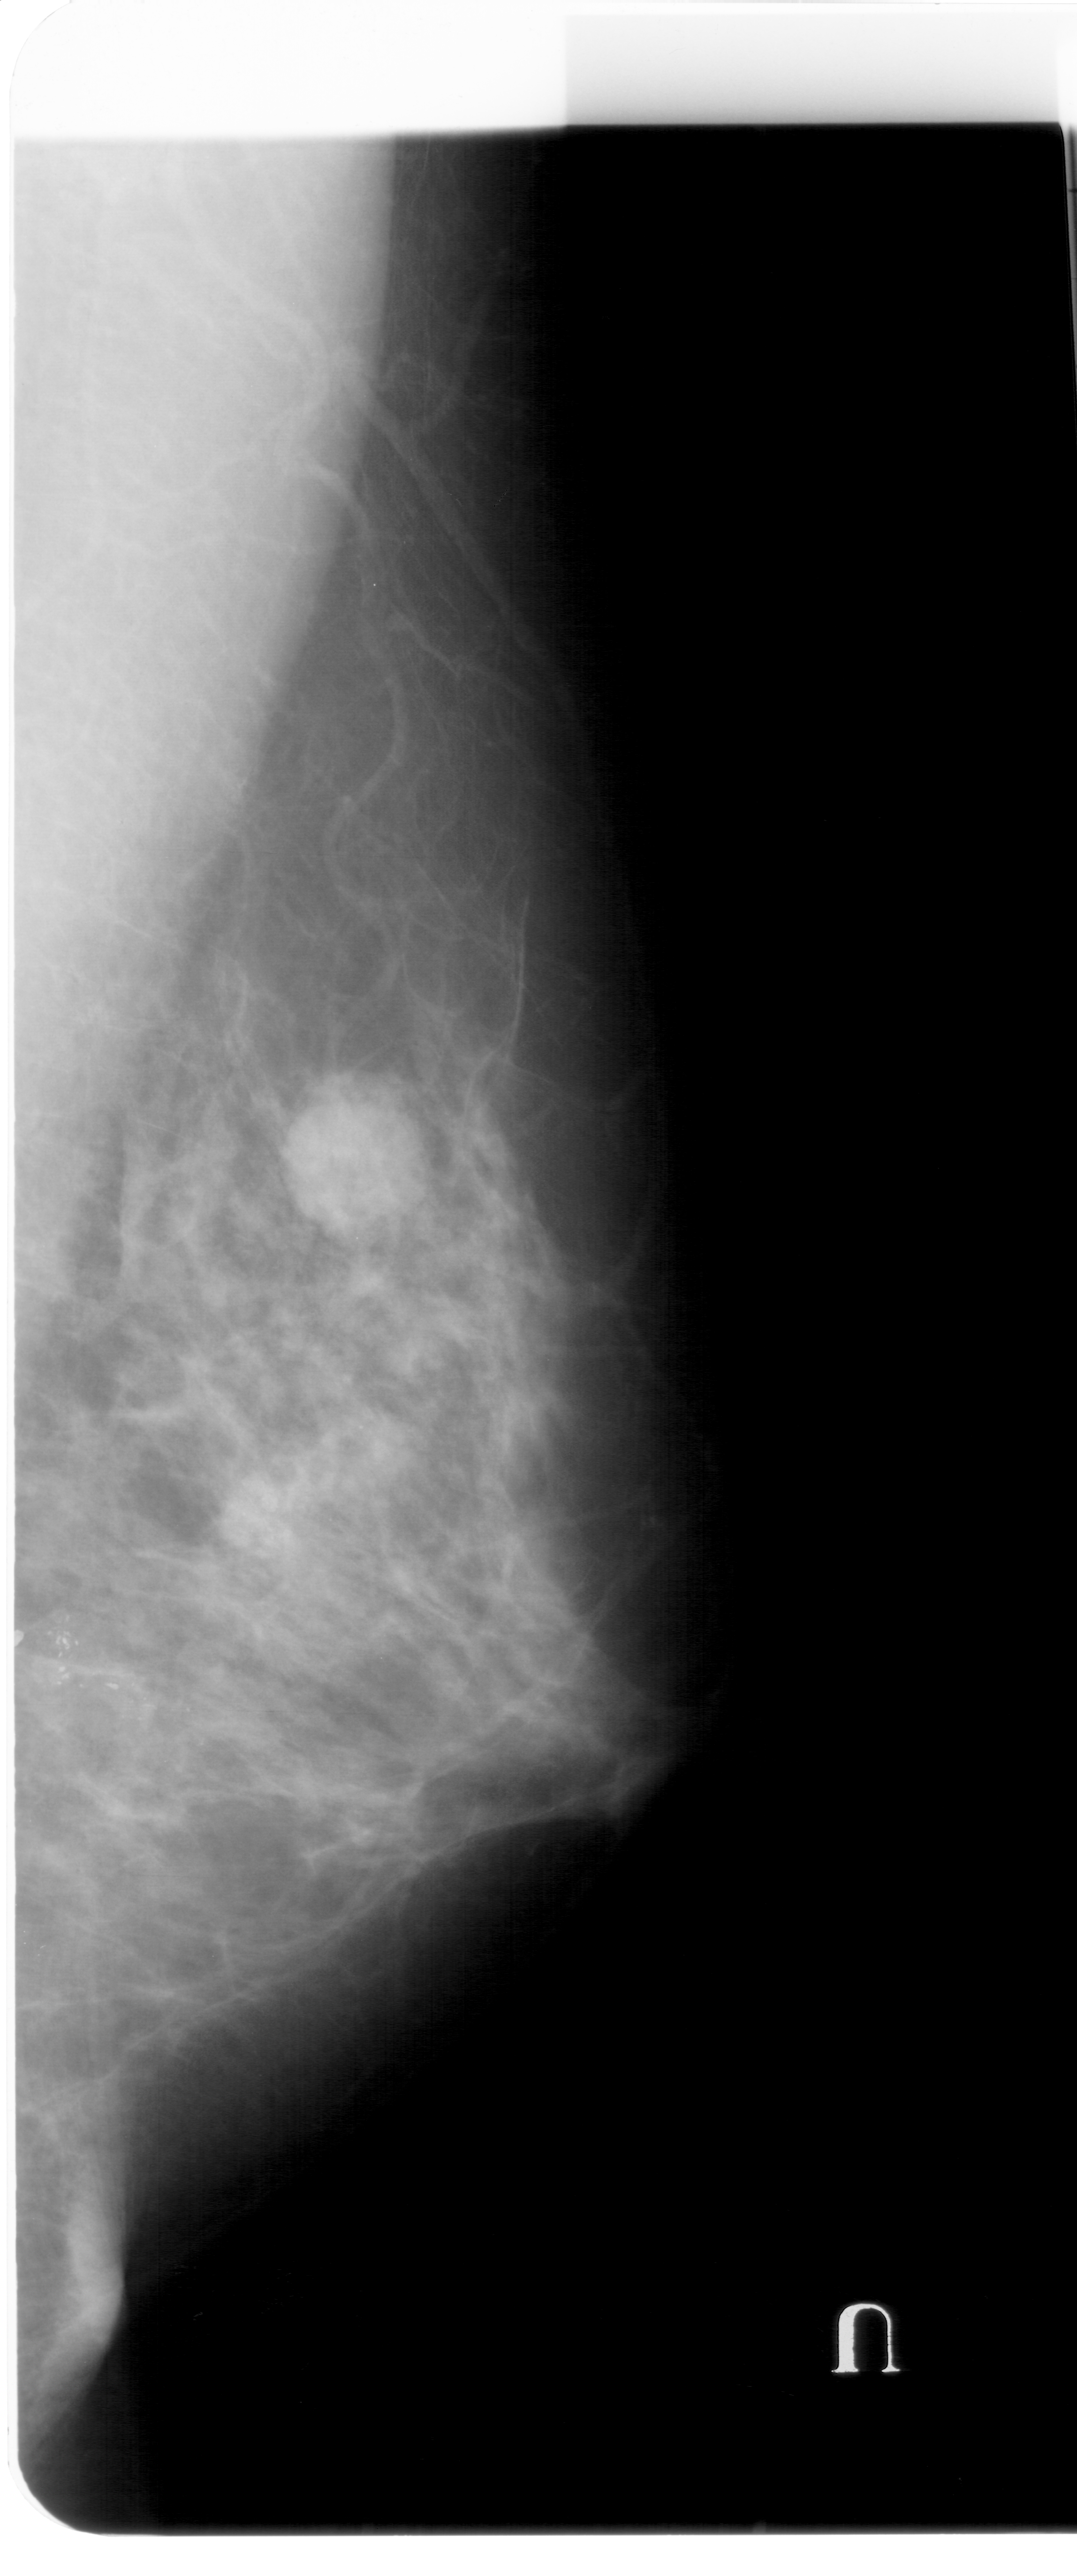
Digitized screen-film mammogram. Right breast. Mediolateral oblique (MLO) view. Breast composition: heterogeneously dense (BI-RADS density category 3 of 4). 1077 × 2576 image matrix.
Expert-marked regions of interest on this image (one box per marked abnormality):
- mass, shape round, margins obscured; BI-RADS assessment category 4; pathology result (as recorded, not read from the image): benign: bounding box (x1, y1, x2, y2) in pixels: (281, 1107, 421, 1242)